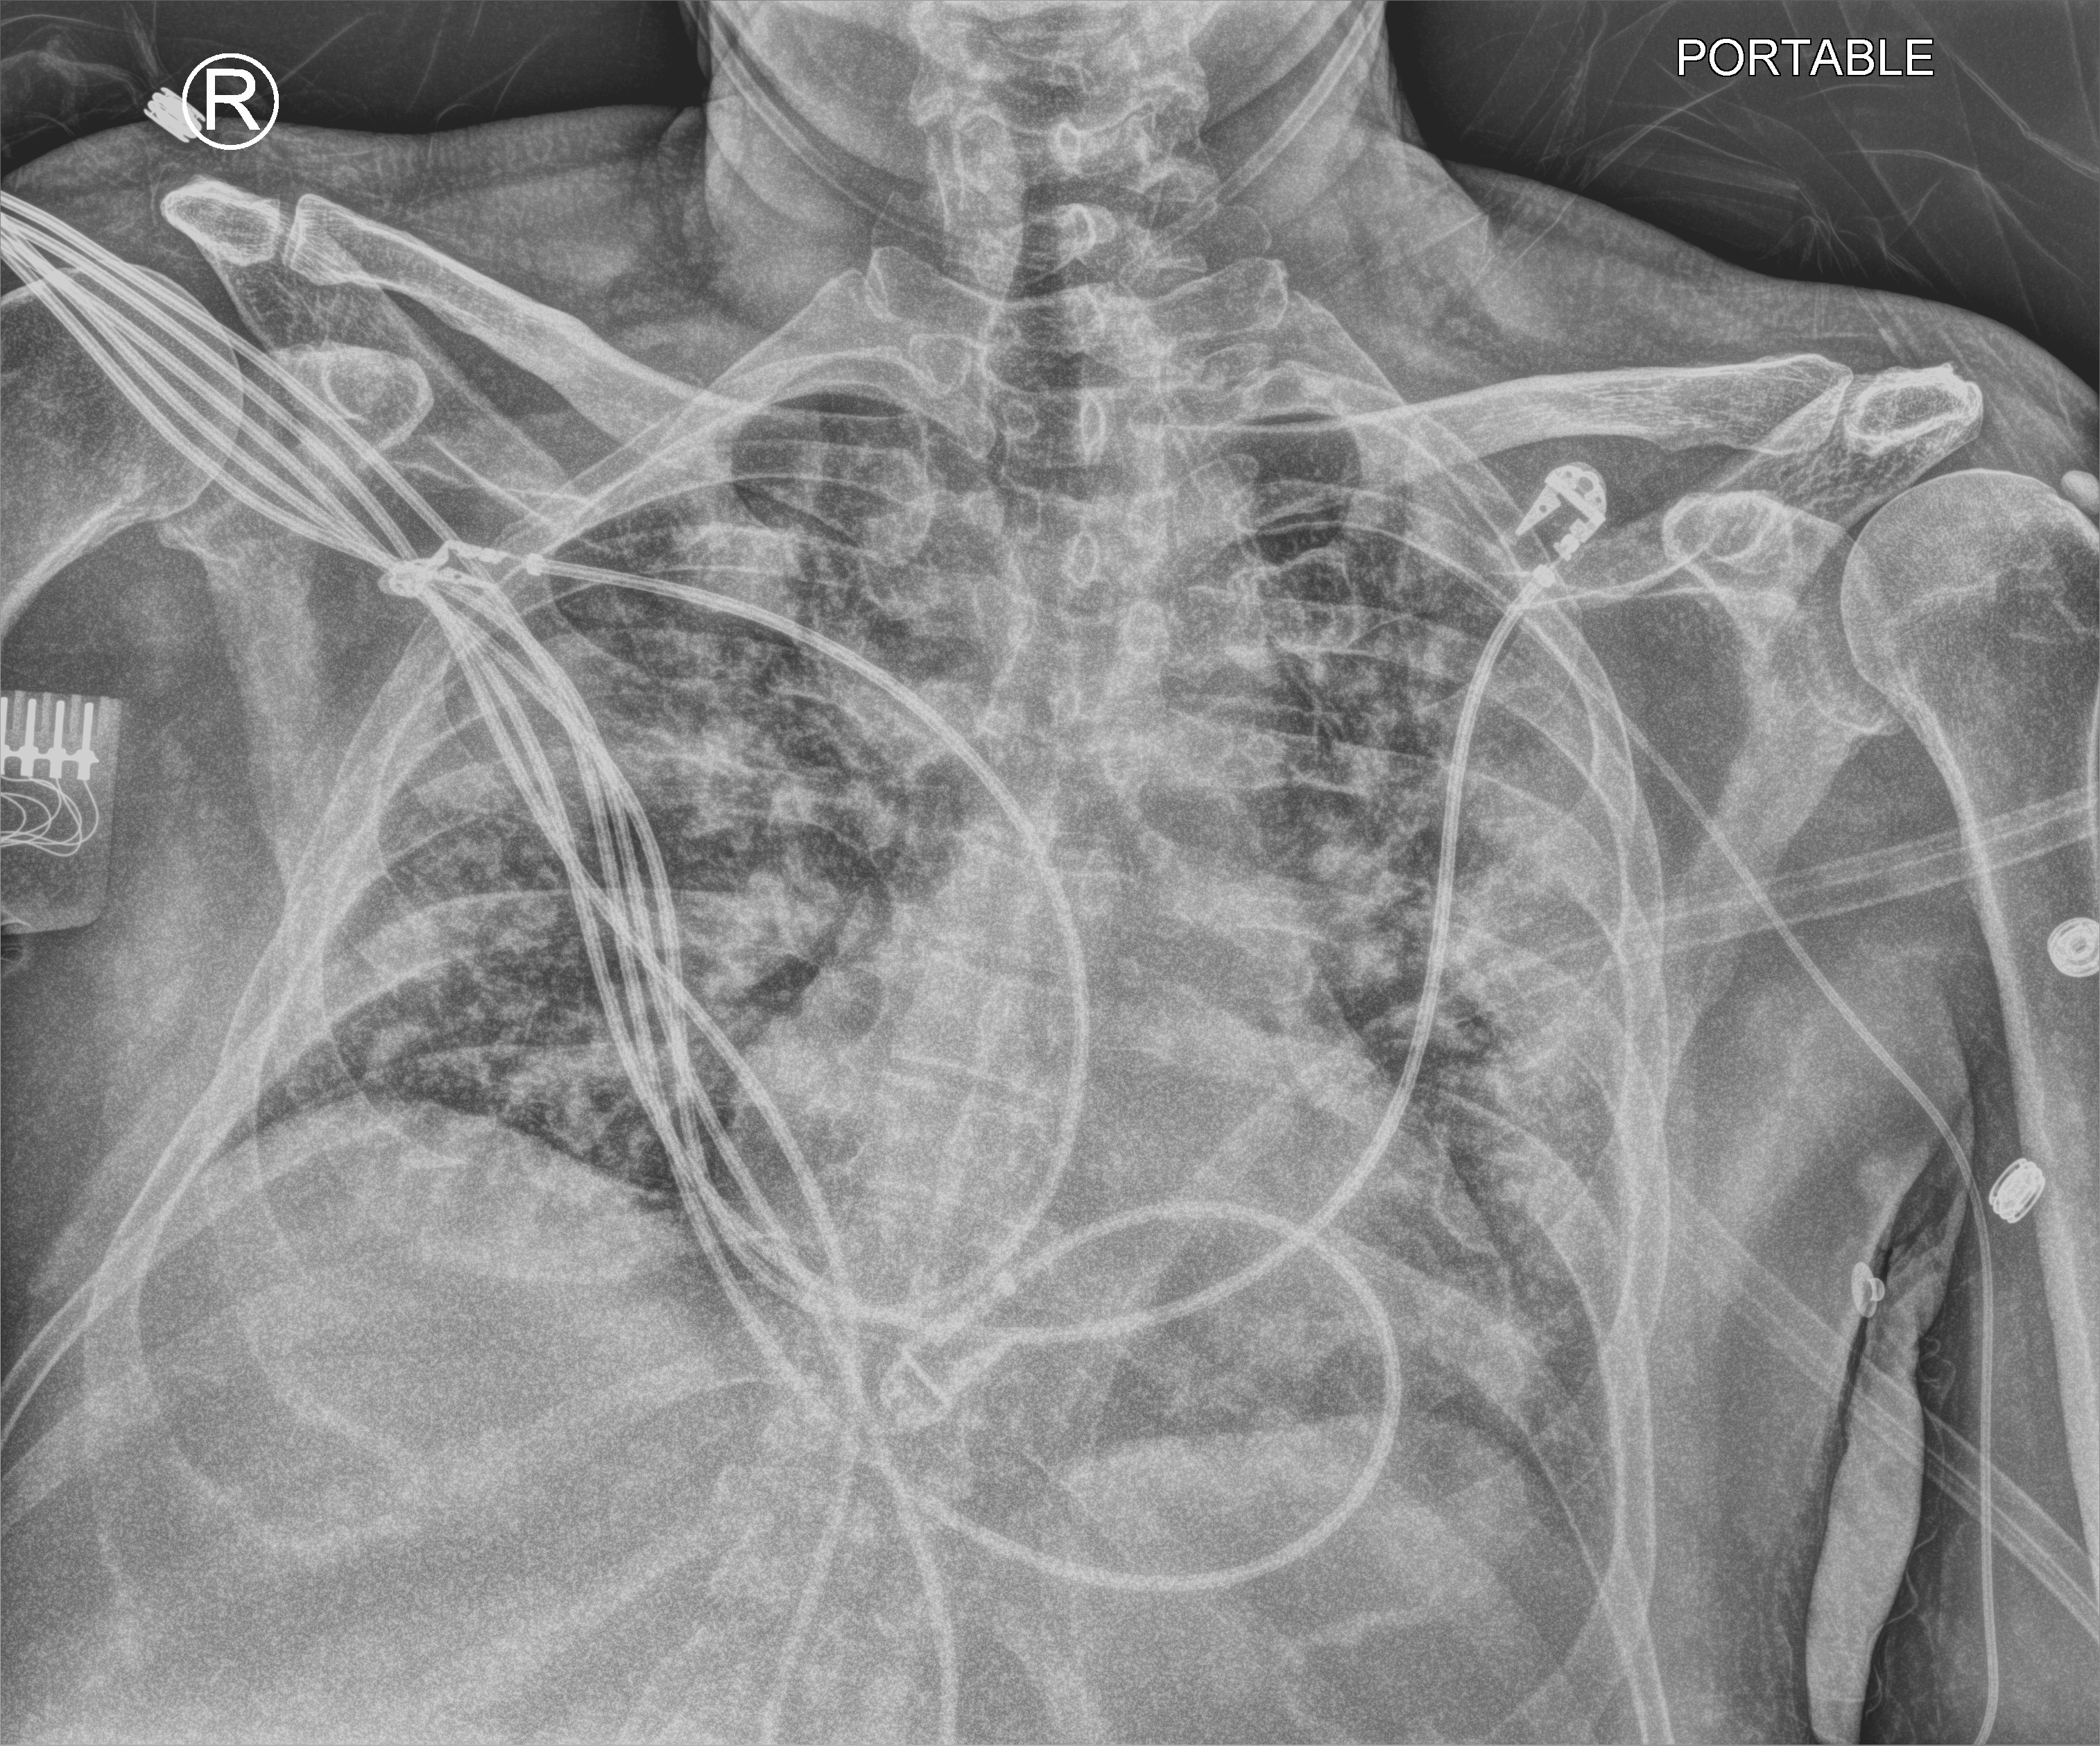
Chest X-ray (portable), anteroposterior (AP) projection. Male patient hospitalised with COVID-19, age 18–59 years.
Hospital-stay facts (about this admission, not read from this image; timing relative to this image not recorded):
- COPD (admission record): no
- other chronic lung disease (admission record): no
- mechanically ventilated during this hospital stay: yes